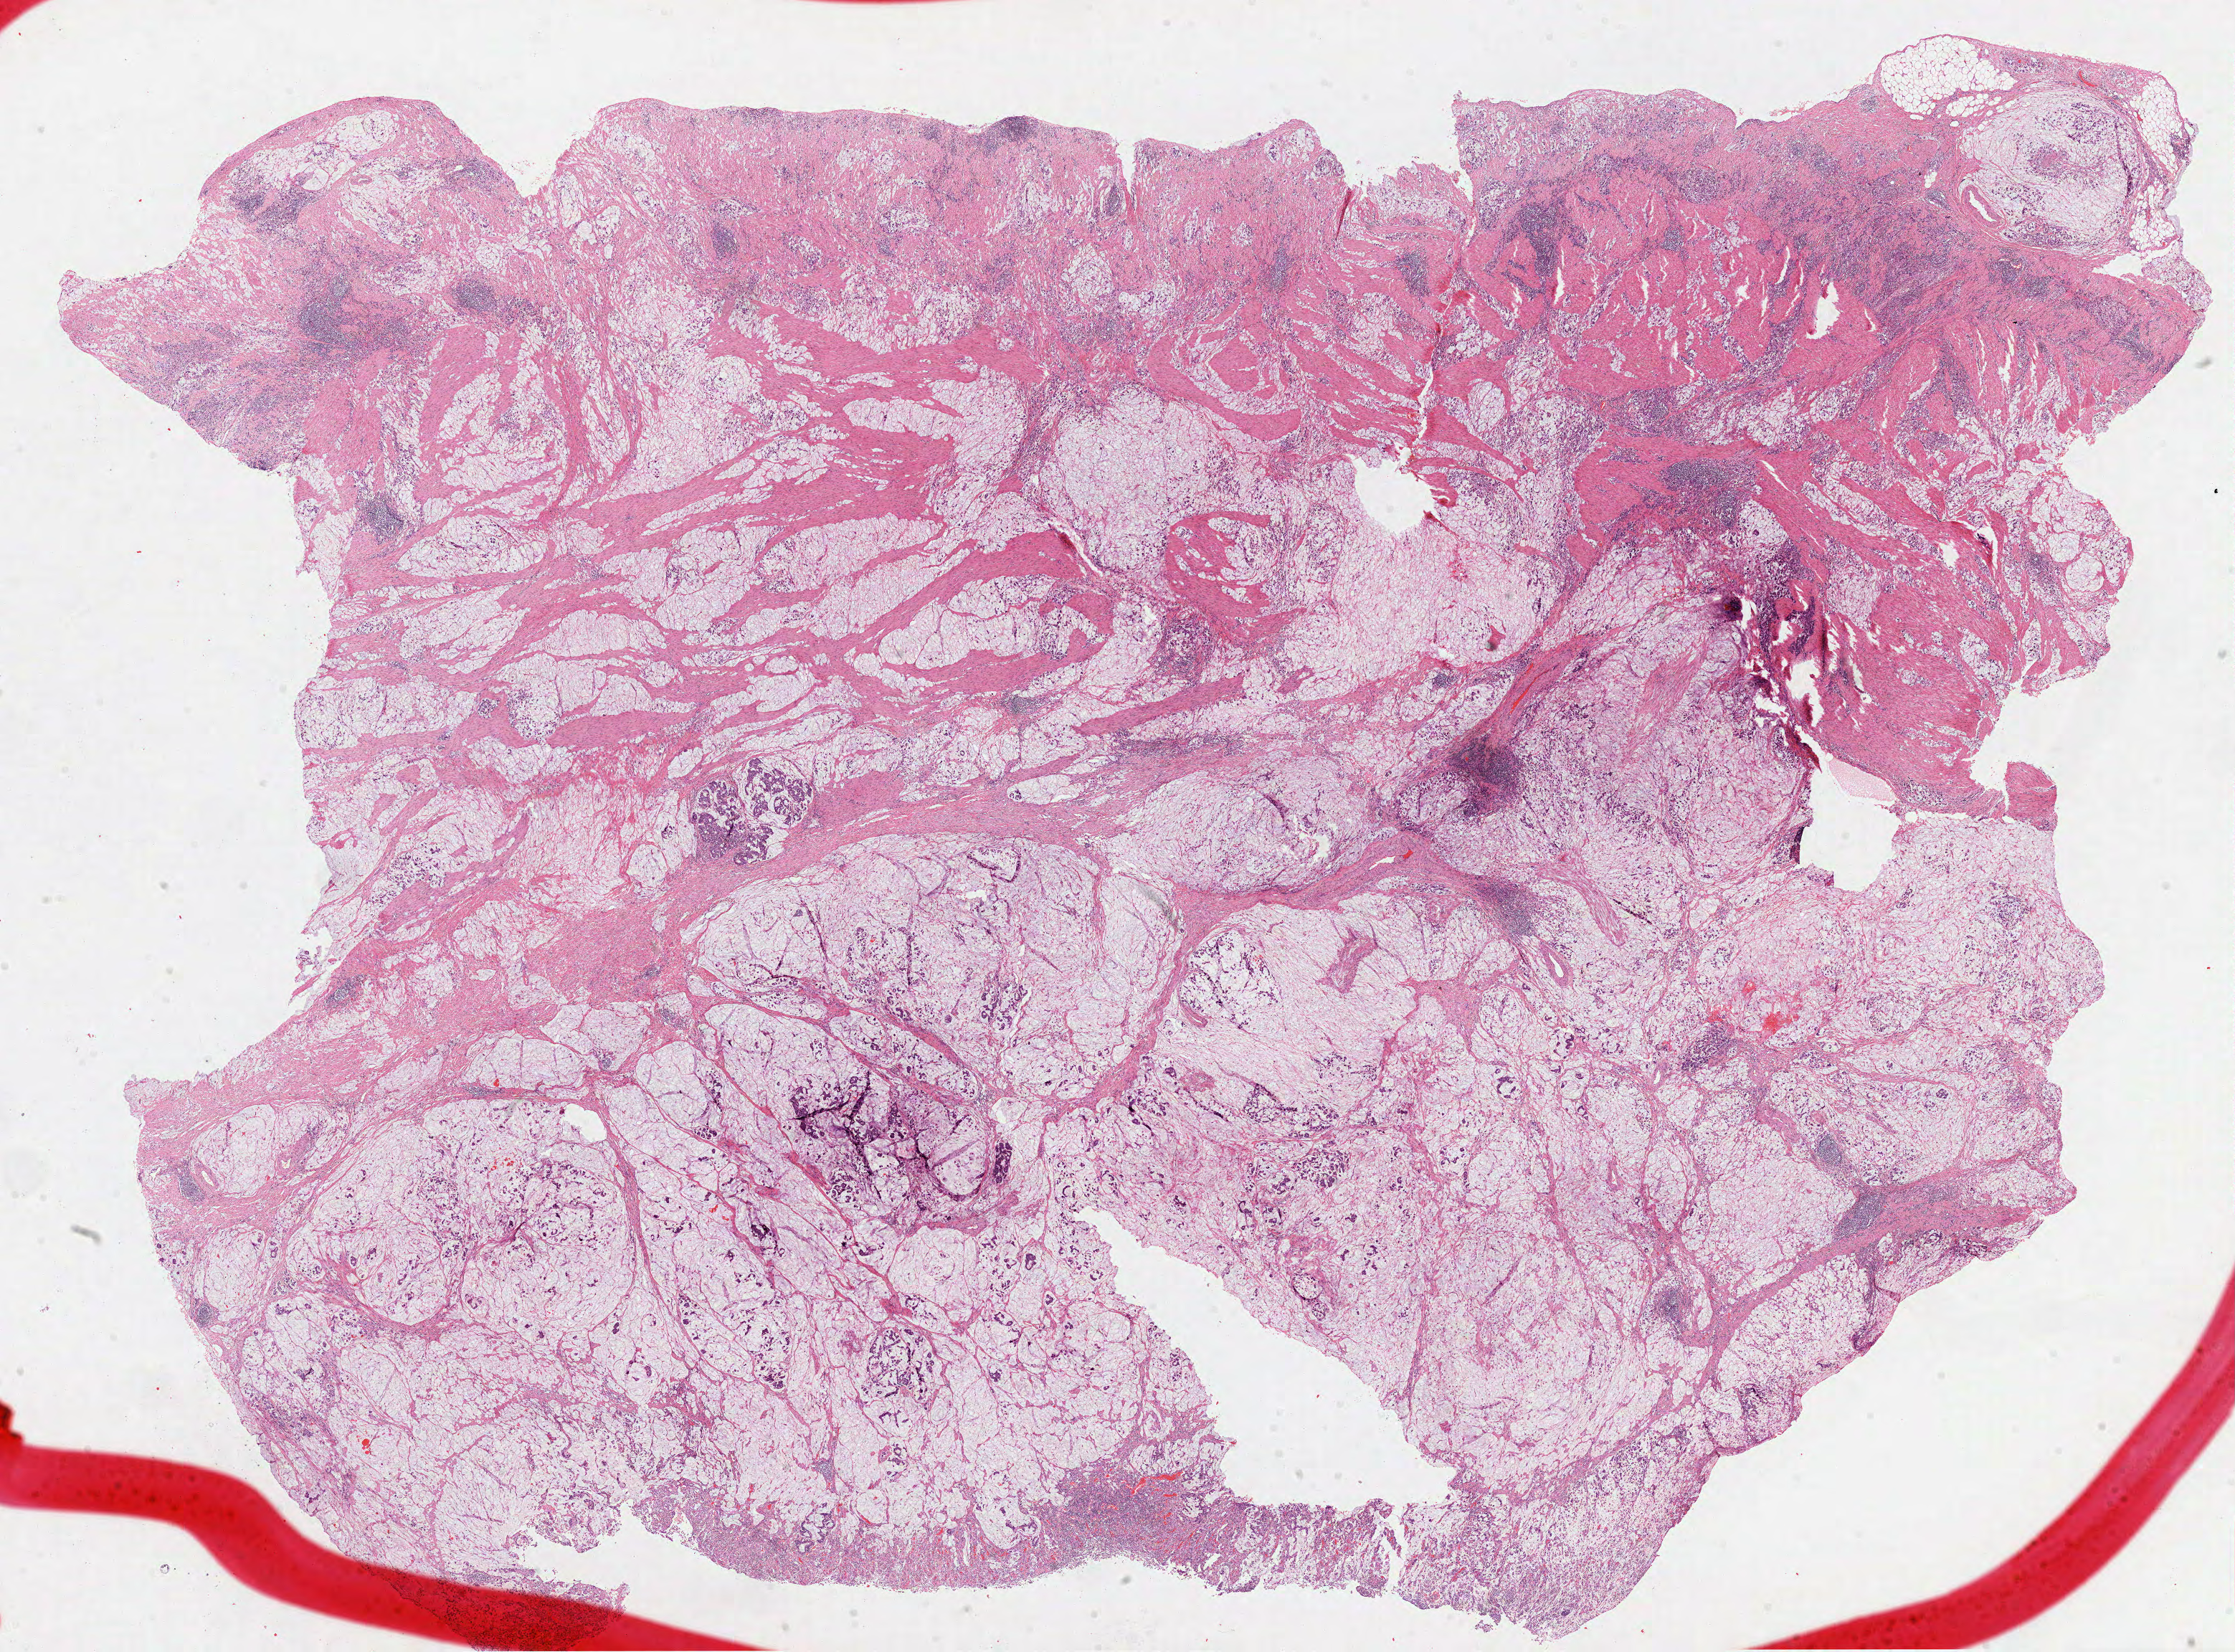
Hematoxylin and eosin (H&E) stained whole-slide image — shown as a low-resolution overview of the whole scanned area (about 25.1 x 18.6 mm). Formalin-fixed paraffin-embedded (FFPE) diagnostic section. Primary tumour sample from the stomach. Female, age 72 years at initial diagnosis.
Diagnosis: Mucinous adenocarcinoma.